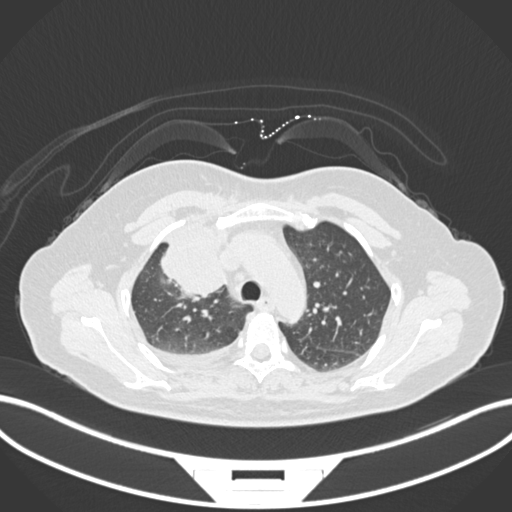
Chest CT, one axial slice. Slice 118 of 172 in the series (ordered by position). Reconstruction kernel B30f. 120 kVp. Lung window (W 1500 / L -600 HU). 1 mm slice thickness. 512 × 512 image matrix, field of view 400 × 400 mm. Female patient, age 52 years. Case-level facts recorded for this patient, not image findings: clinical TNM (as recorded): T3 N1 M1.
Annotated regions visible in this slice (bounding box drawn by a radiologist):
- lung tumour (recorded histology: adenocarcinoma): bounding box [x1, y1, x2, y2] px = [160, 223, 237, 303]